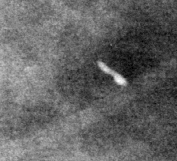
Crop from a digitized film mammogram around one marked abnormality; left breast; CC view; BI-RADS breast density category 1 (scale 1–4).
Finding: calcifications, distribution regional; BI-RADS assessment category 2; subtlety rating 3 on a 1 (subtle) to 5 (obvious) scale; benign; no additional work-up was recommended (benign without callback).